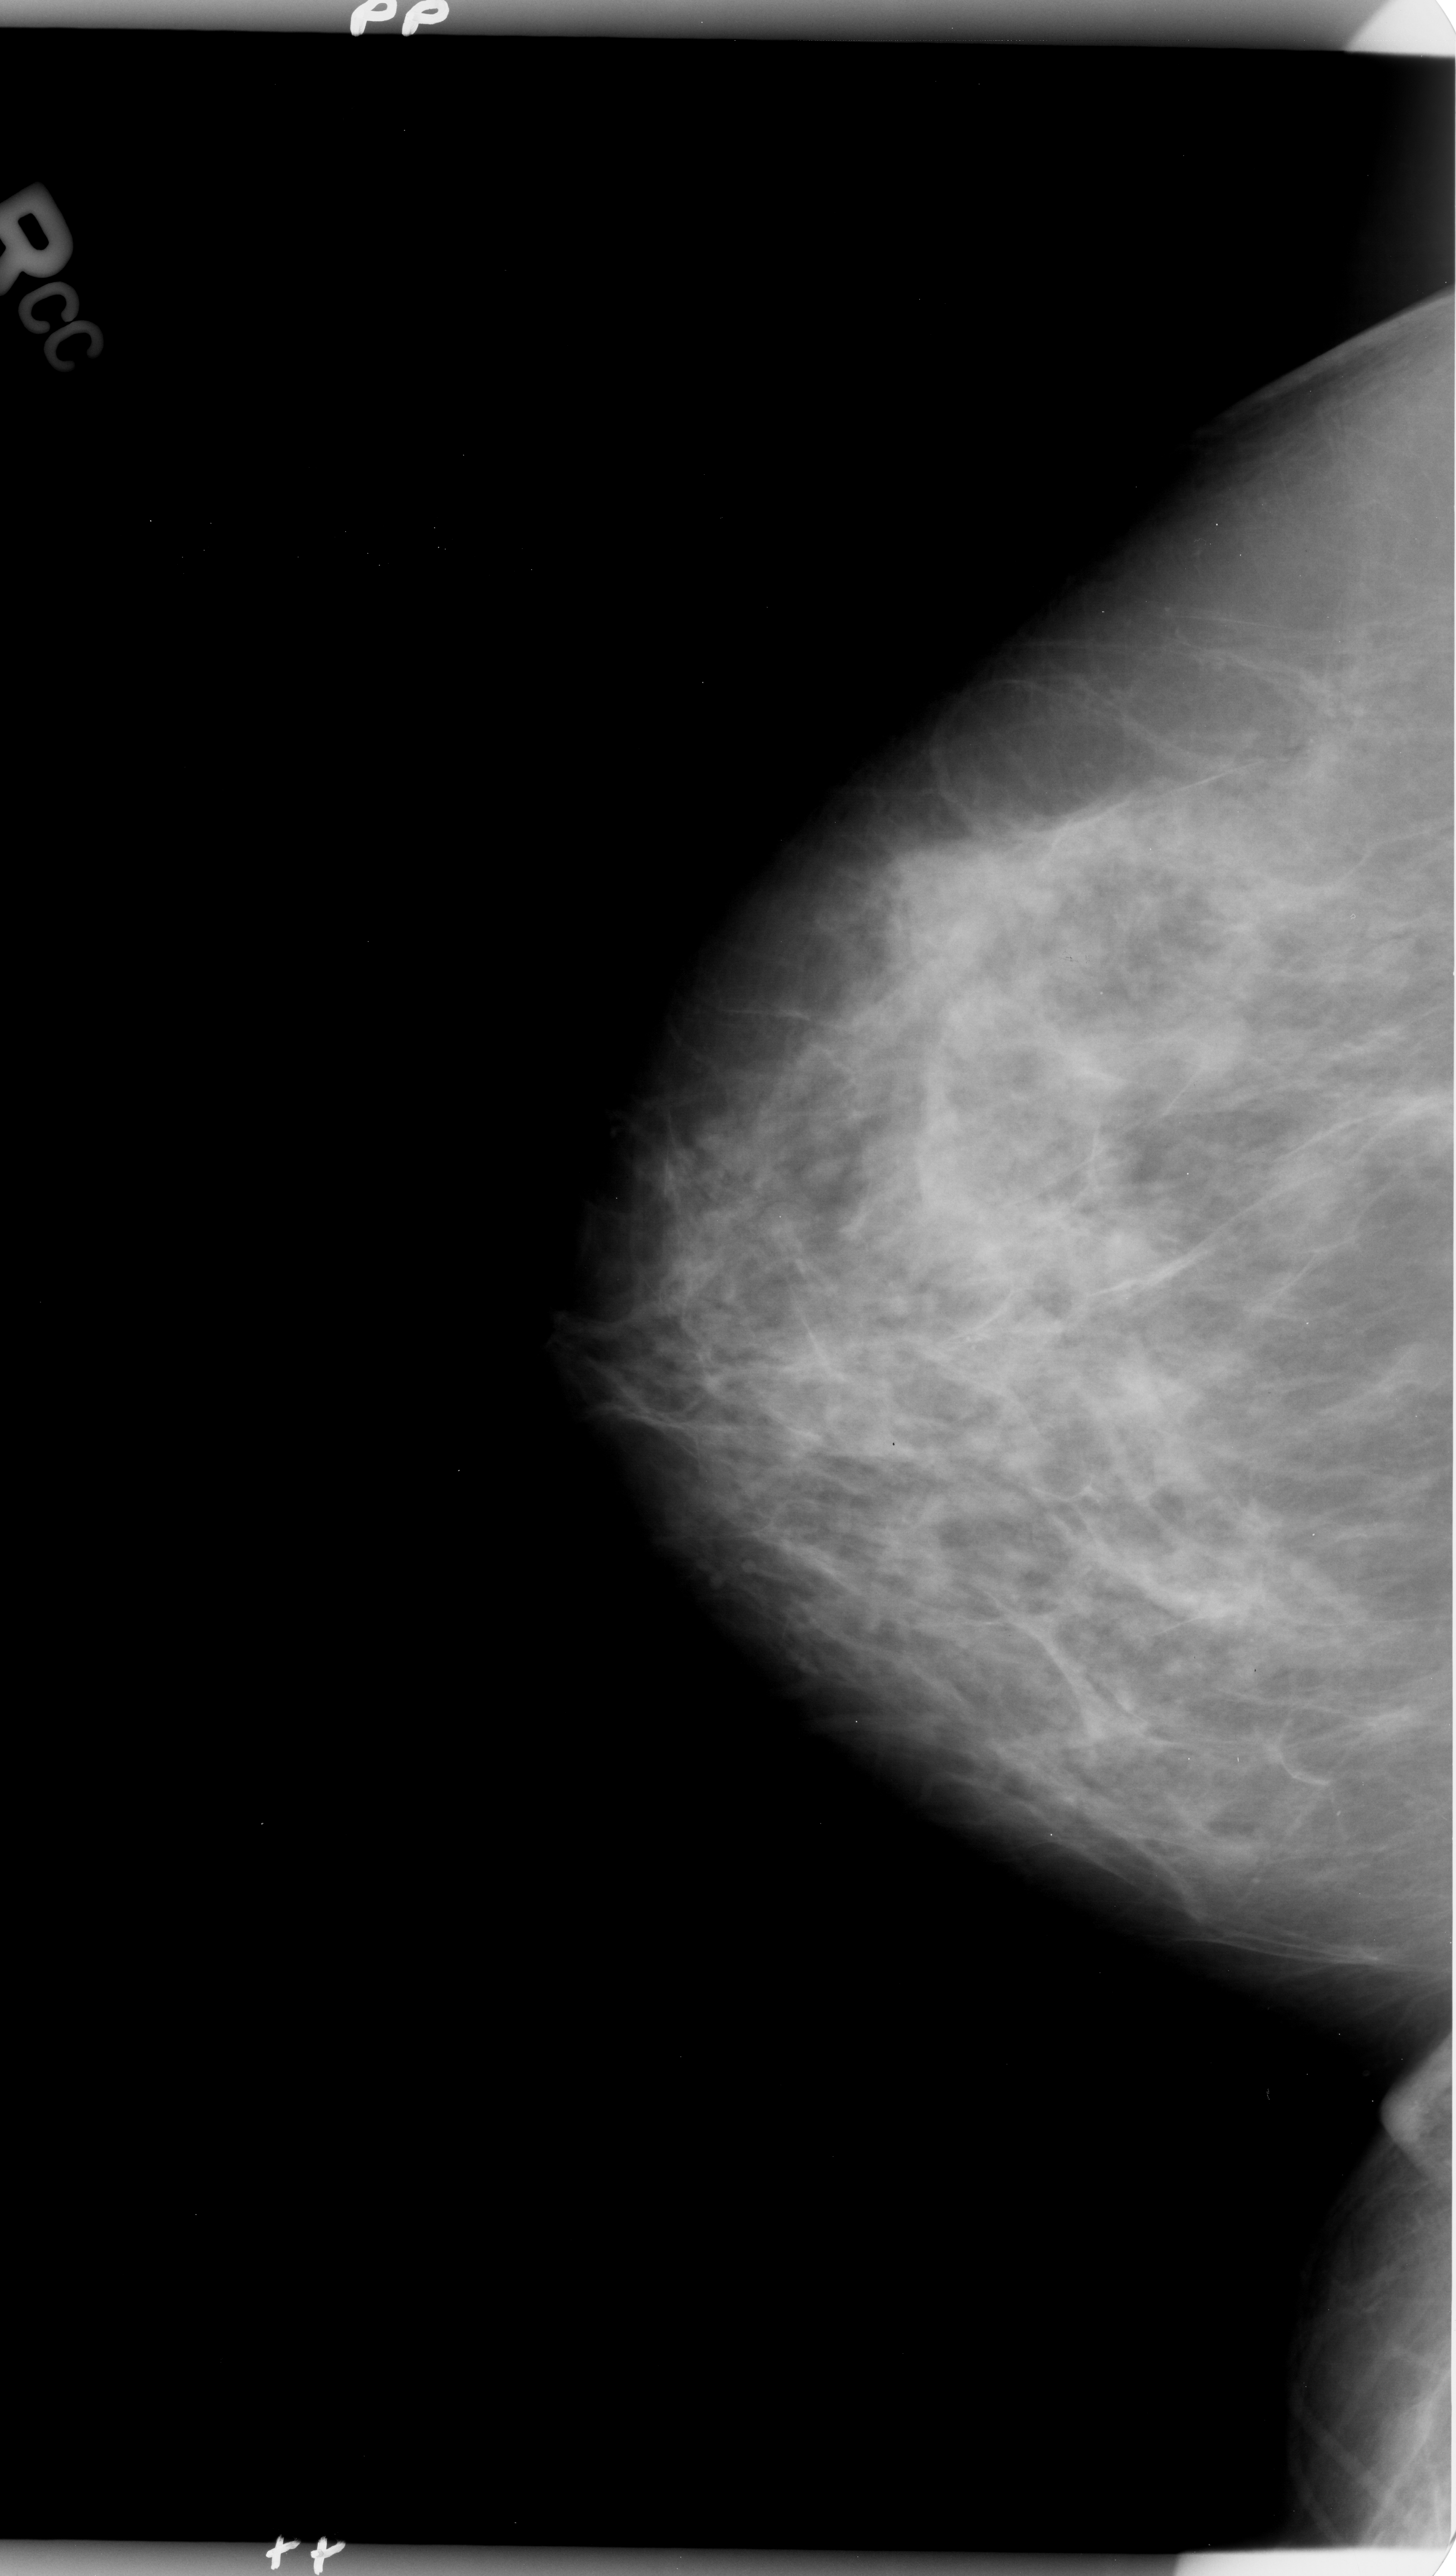
Mammogram (digitized film). Right breast. Craniocaudal (CC) view. 1456 × 2576 image matrix.
Marked abnormalities (boxes around the expert regions of interest):
- Finding 1 of 2: calcifications, morphology amorphous / pleomorphic, distribution clustered; BI-RADS assessment category 4; pathology result (as recorded, not read from the image): benign: box from (x=945, y=1295) to (x=1012, y=1376) px
- Finding 2 of 2: calcifications, morphology amorphous / pleomorphic, distribution clustered; BI-RADS assessment category 4; pathology (as recorded): benign: (x=1277, y=714)–(x=1348, y=799)